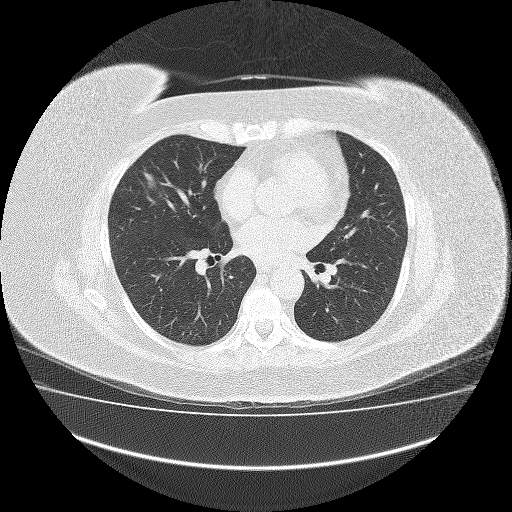
Low-dose screening chest CT, axial slice, third annual screen, lung window (W 1500 / L -600 HU), 2 mm slice thickness, slice 80 of 162 in the series, 512 × 512 image matrix, field of view 420 × 420 mm. Female participant, aged 64 years at enrolment. Former smoker at enrolment.
Lesion marked by an expert reader, bounding box (x1, y1, x2, y2) in pixels: (133, 166, 189, 209). The exam's reader record, not a measurement of the box and not confirmed to be the same lesion: non-calcified nodule or mass ≥4 mm, right middle lobe, 23 × 13 mm, smooth margins, soft tissue attenuation, pre-existing on the prior screen: no.